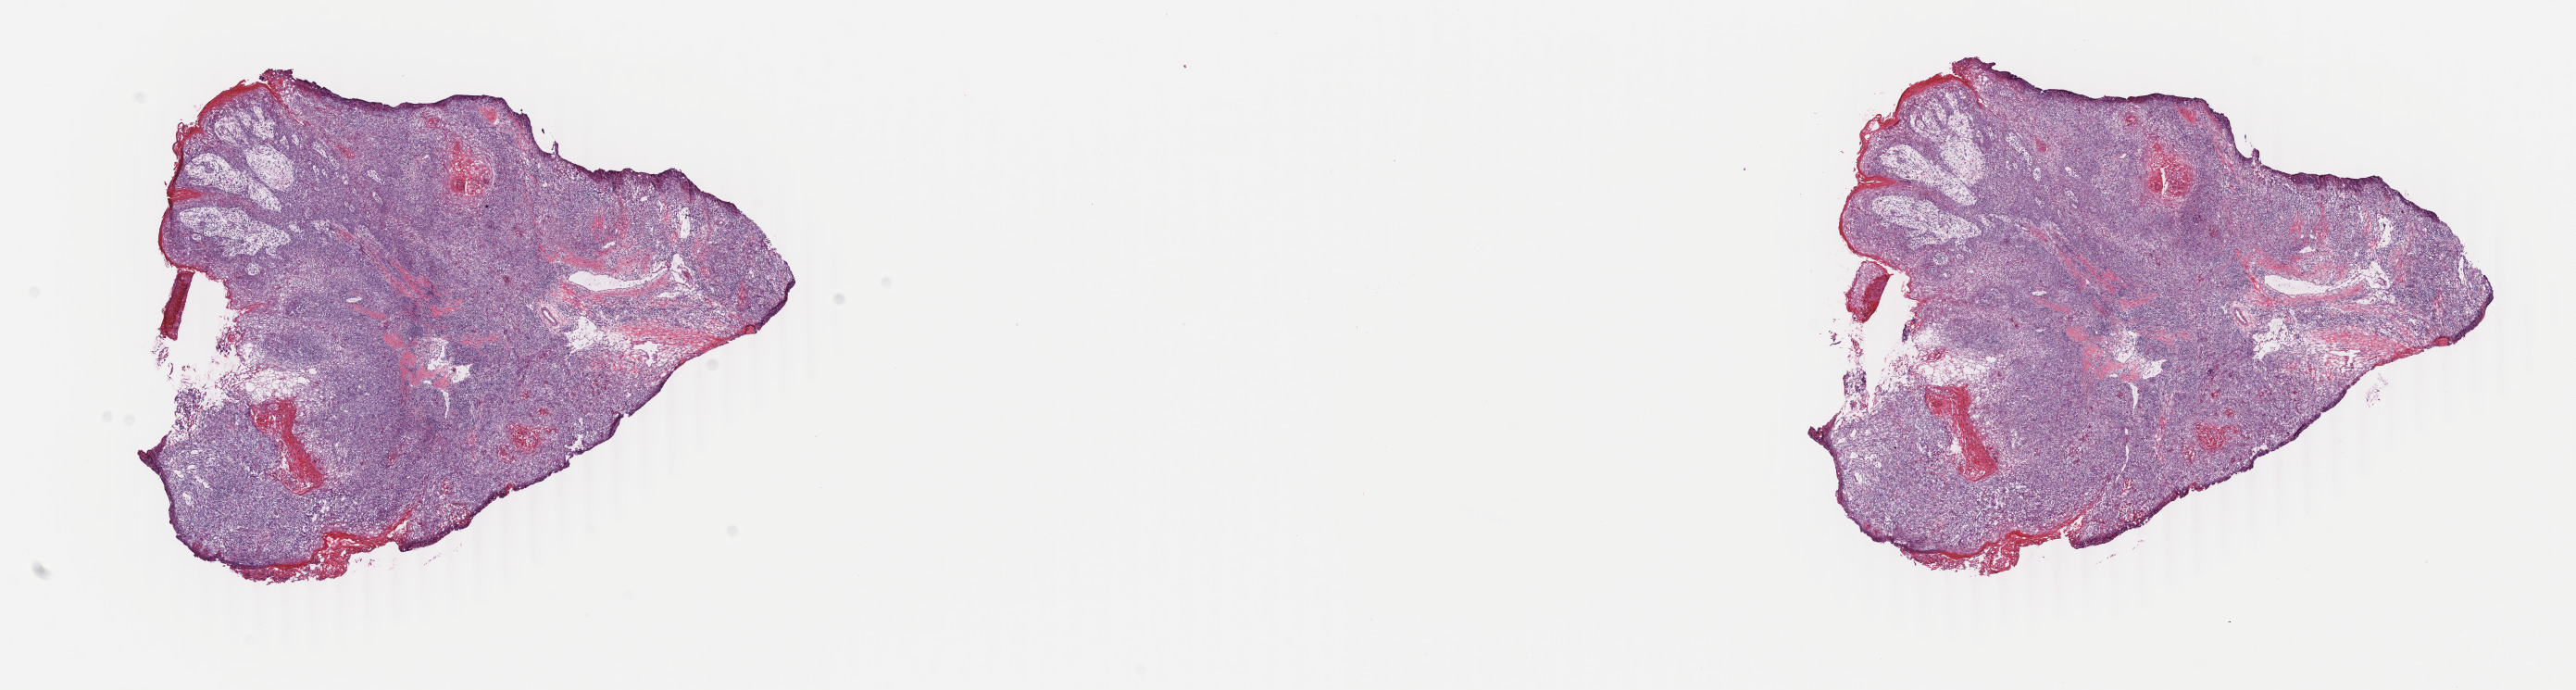
Whole-slide histology image, Hematoxylin and eosin (H&E) stained, low-resolution overview of the scanned area, about 22.1 x 5.9 mm (slide scanned at 40x), frozen section from the top of the tissue portion, head and neck, primary tumour sample. Female patient; age at initial diagnosis 72 years. Histologic grade: G3 (poorly differentiated). Composition of this section per pathologist review: tumour cells 80%, tumour nuclei 80%, normal cells 0%, stromal cells 10%, necrosis 10%. Inflammatory infiltration, as recorded: lymphocyte infiltration 40%, monocyte infiltration 20%, neutrophil infiltration 20%.
- AJCC pathologic stage: IVA (6th edition)
- histologic diagnosis: Squamous cell carcinoma, NOS (floor of mouth, NOS)